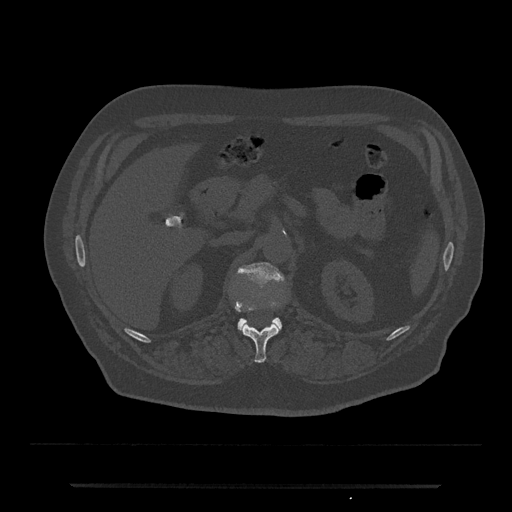
CT including the spine, one axial slice; position 571 of 797 along the scan axis; 120 kVp; bone window (W 1800 / L 400 HU); 0.5 mm slice thickness; 512 × 512 image matrix, field of view 434 × 434 mm. Patient: male, 80 years. Case-level facts recorded for this patient, not image findings: primary cancer: prostate; vertebrae with lytic lesions (as recorded): L1, T11.
Annotated regions visible in this slice (semi-automatically segmented with operator editing):
- L1 vertebra: bounding box (x1, y1, x2, y2) in pixels: (237, 262, 285, 332)
- T12 vertebra: (235, 303, 280, 363)